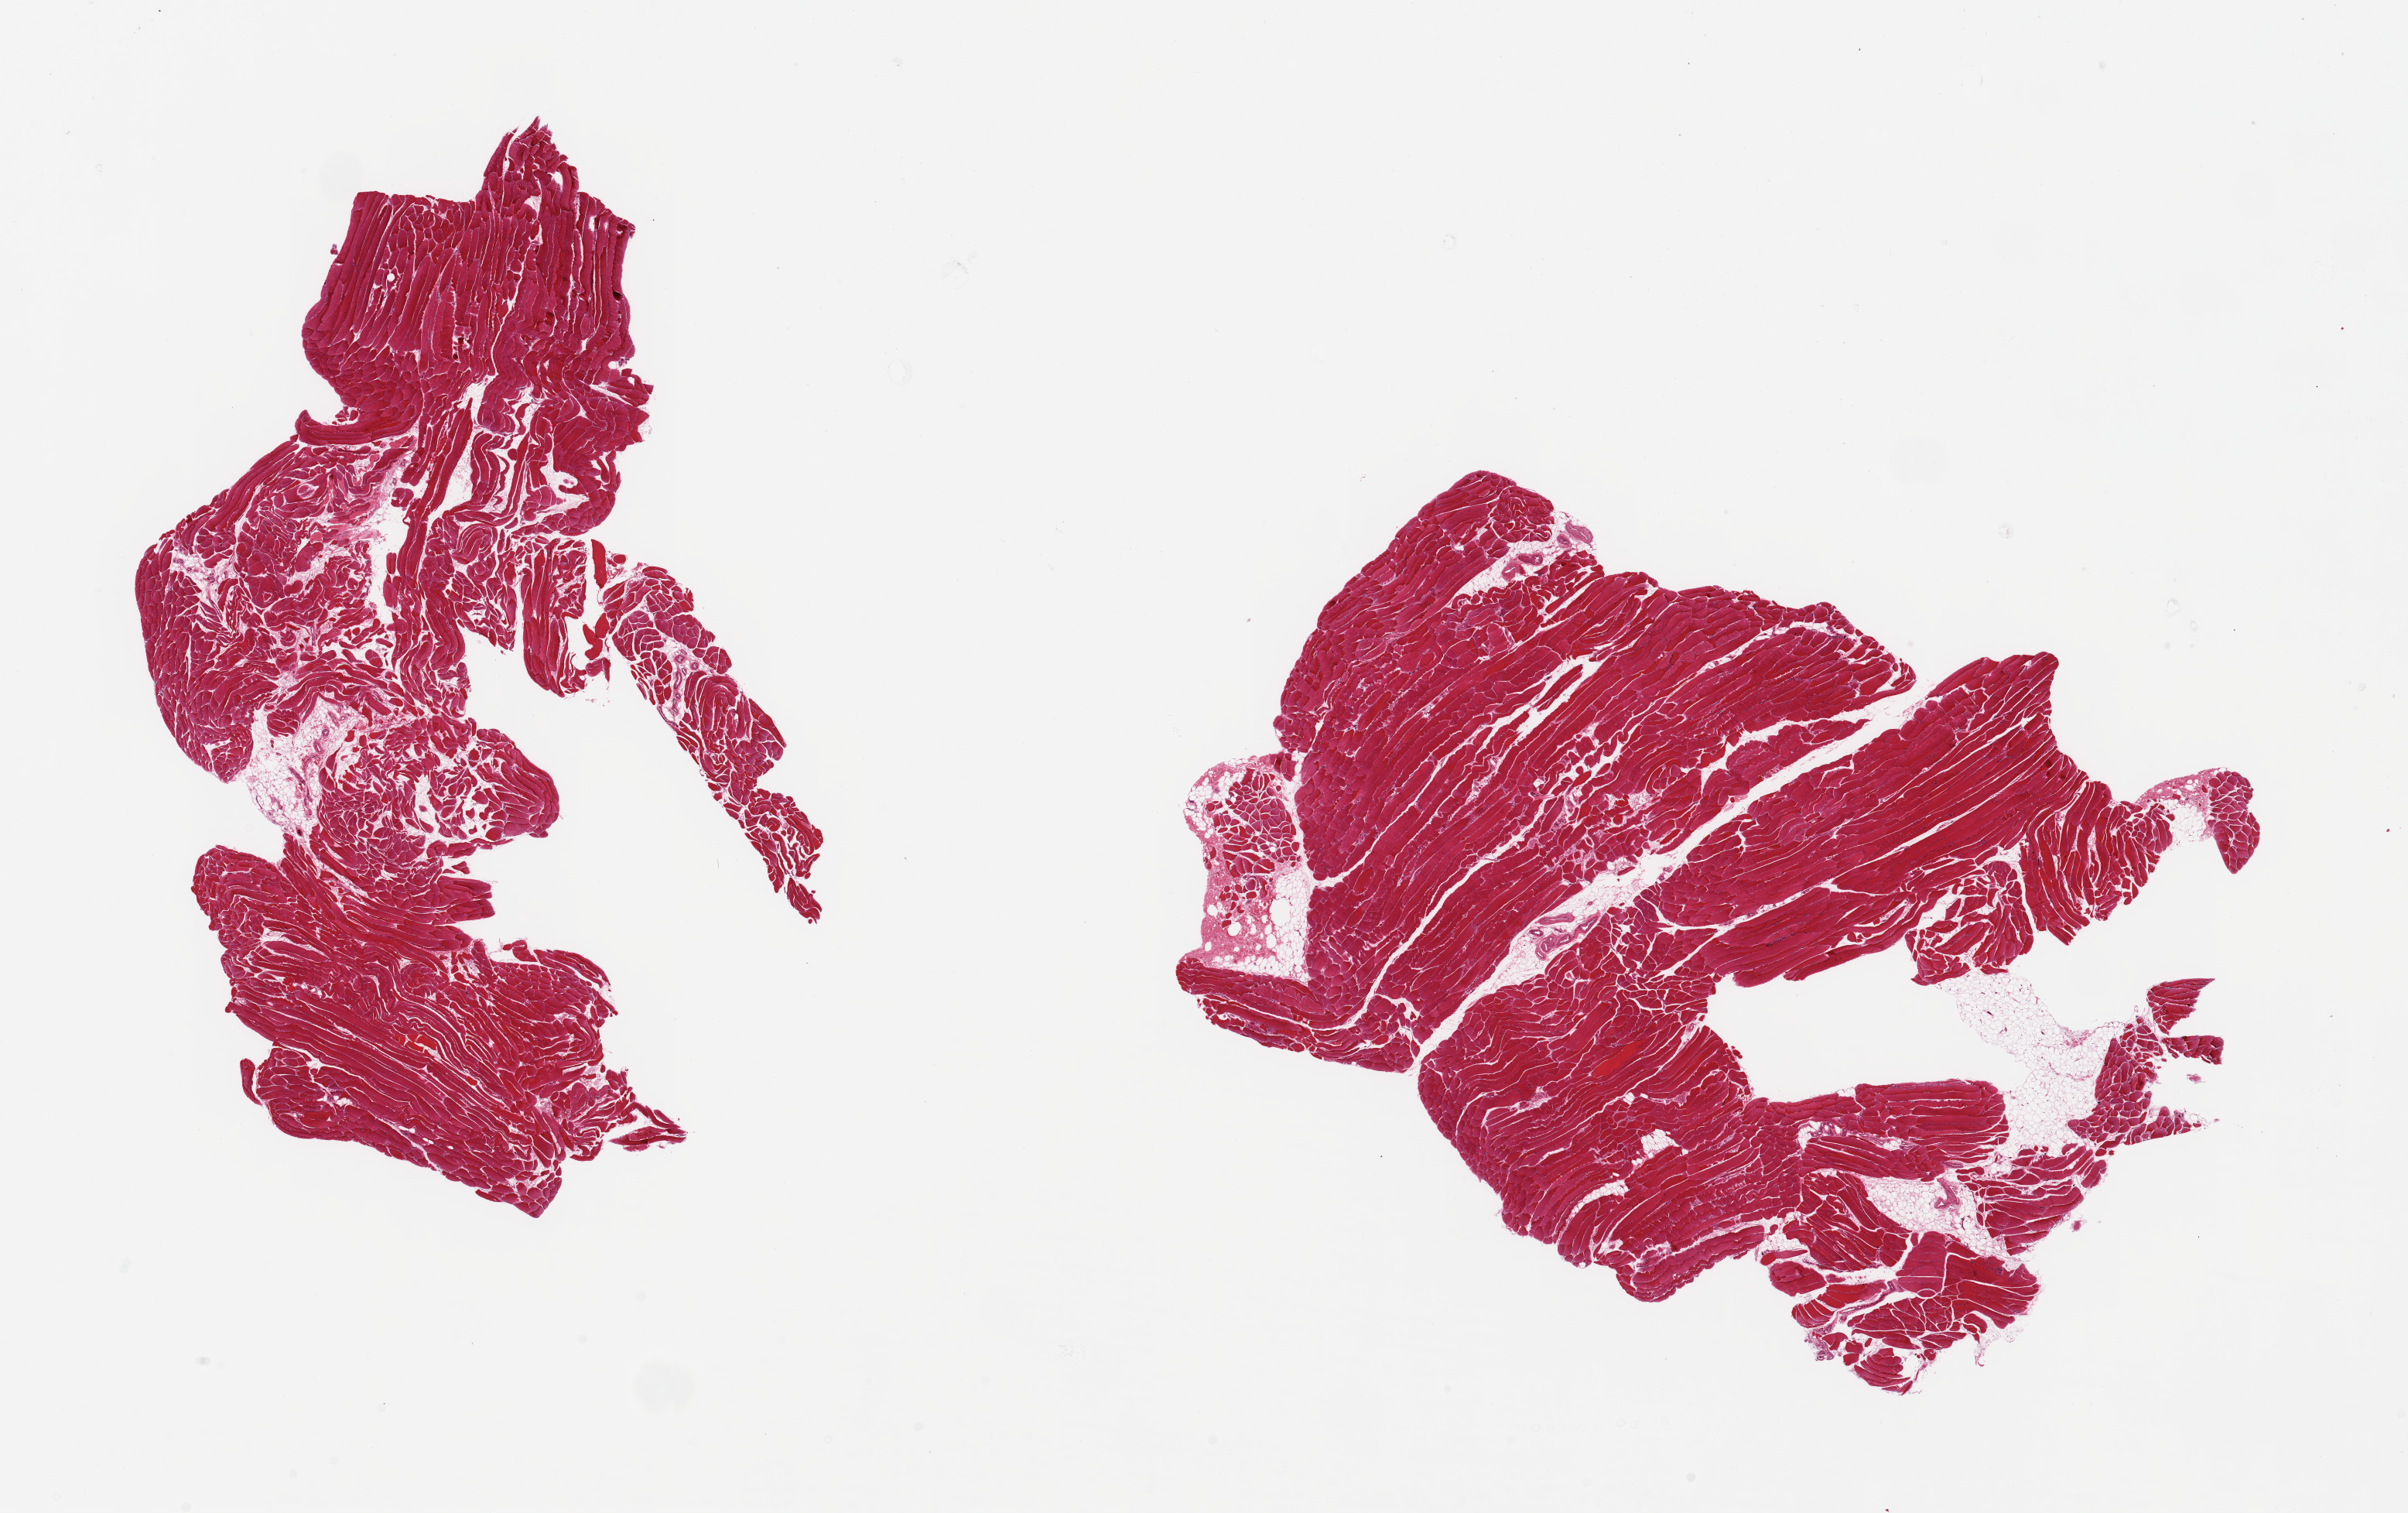
Whole-slide image, haematoxylin and eosin stain, whole scanned area (about 24.6 x 15.5 mm, acquisition: 20x scan) shown as a low-resolution overview. PAXgene-fixed, paraffin-embedded tissue. Target tissue: skeletal muscle. Tissue donor sample. Donor: male.
Review note (as recorded): 2 pieces; 5% fat content.